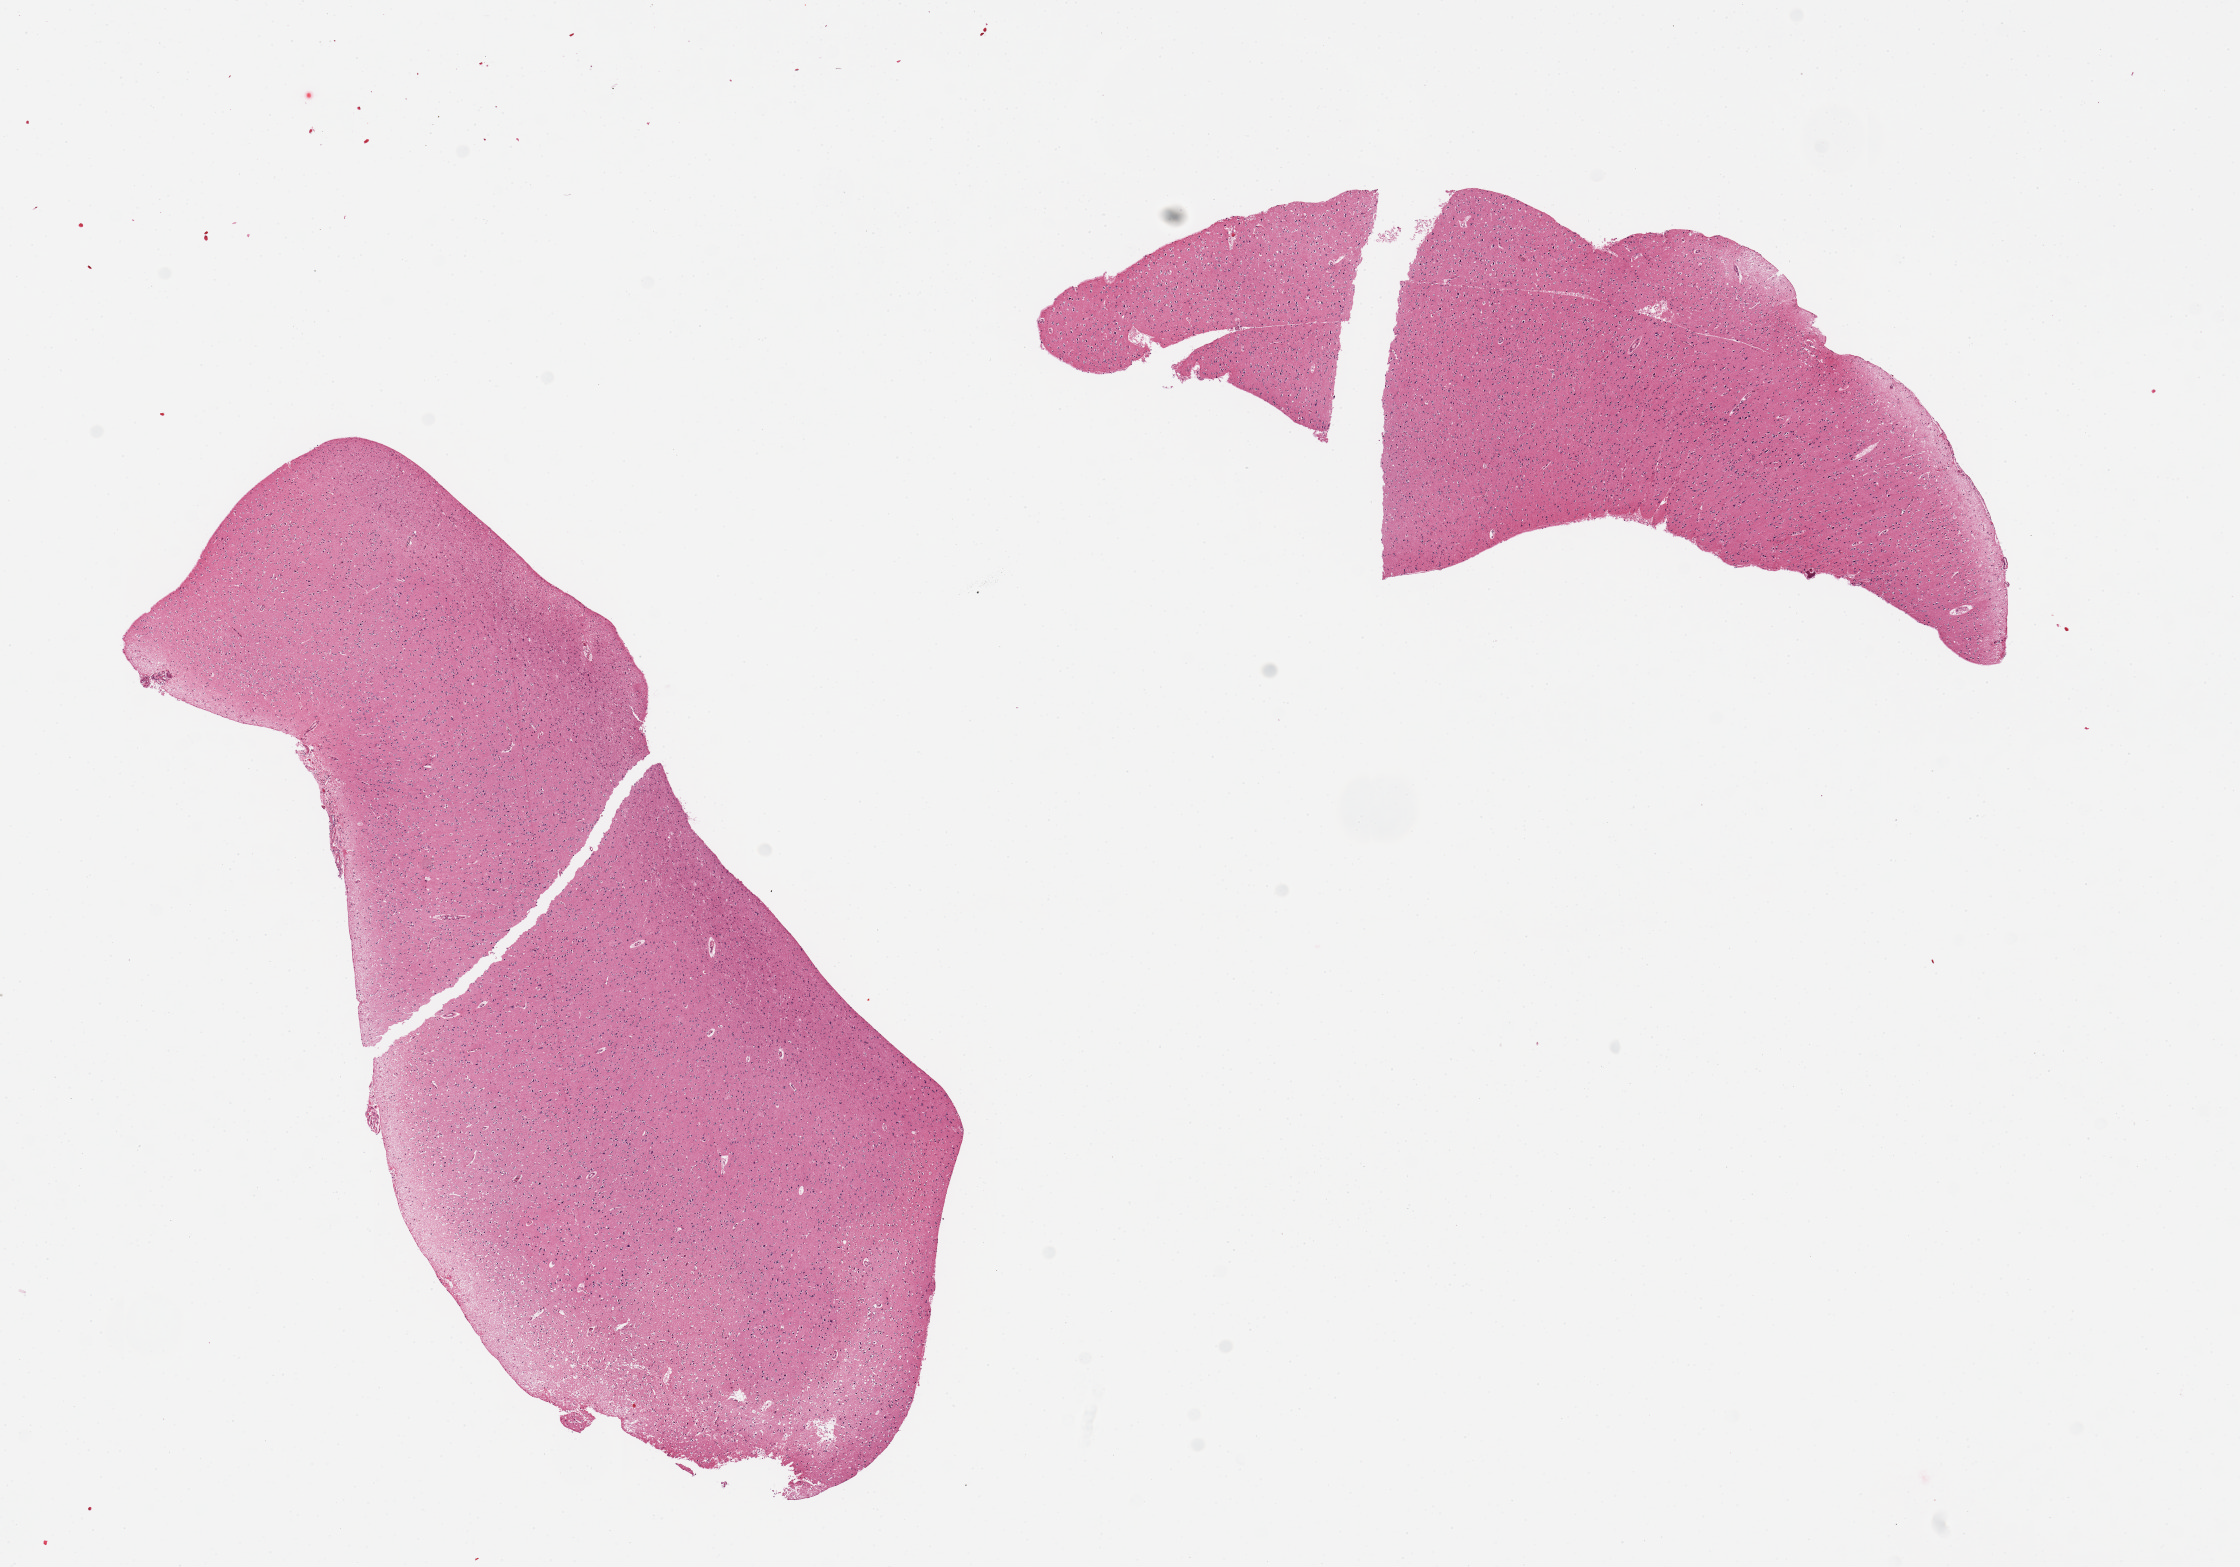
Digitized H&E-stained section — a low-resolution overview of the entire scanned area, about 17.7 x 12.4 mm; PAXgene-fixed paraffin-embedded (PFPE) section; sampled site (target tissue): cerebral cortex; tissue donor sample.
- review note (as recorded): 2 pieces